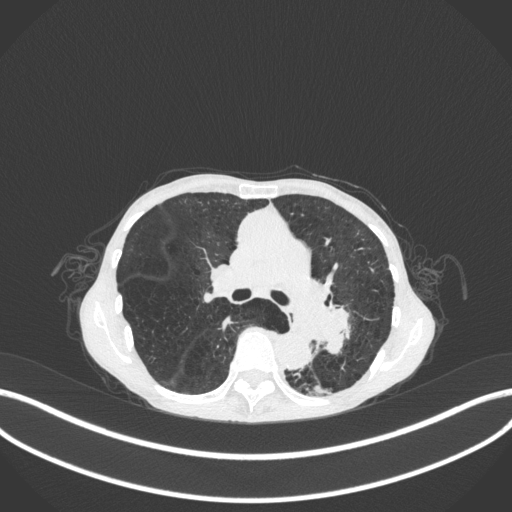
Chest CT, one axial slice; position 170 of 347 along the scan axis; reconstruction kernel B31f; 120 kVp; lung window (W 1500 / L -600 HU); 1 mm slice thickness; 512 × 512 image matrix, field of view 400 × 400 mm. Patient: female, 70 years. From the clinical record (not read from this slice): clinical TNM (as recorded): T3 N0 M0.
Annotated regions visible in this slice (rectangle marked by the reading radiologist):
- lung tumour (recorded histology: small cell carcinoma): bounding box (x1, y1, x2, y2) in pixels: (312, 293, 358, 364)